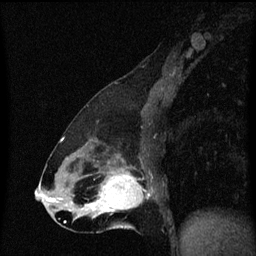
Breast MRI (dynamic contrast-enhanced), one sagittal slice. Slice 29 of 60 in the series (ordered by position). Dynamic contrast-enhanced series, image 2 of 3 at this slice position (ordered by acquisition). 1.5 T. TE 4.2 ms, TR 8.4 ms. 2 mm slice thickness. 256 × 256 image matrix, field of view 200 × 200 mm. Patient: female, 47 years.
Annotated regions visible in this slice (semi-automatic segmentation, software-assisted and operator-edited):
- analysis volume of interest (the breast-tissue region the enhancement analysis was run in; not a lesion): bounding box [x1, y1, x2, y2] px = [100, 172, 151, 219]
- tumour enhancement mask (voxels above the 70 % enhancement threshold inside the analysis volume of interest): [100, 172, 144, 213]